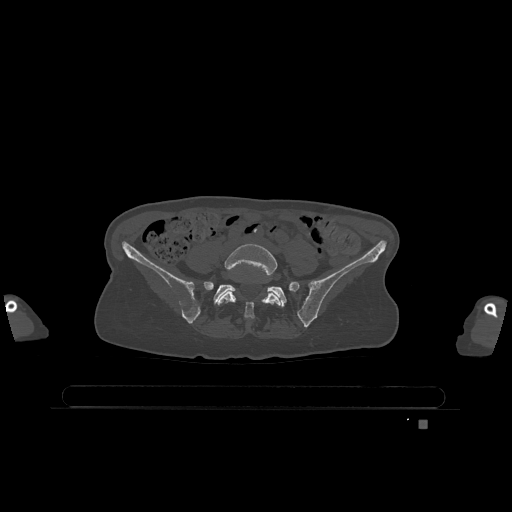
CT including the spine, one axial slice; slice 221 of 1317 in the series (ordered by position); bone window (W 1800 / L 400 HU); 512 × 512 image matrix, field of view 500 × 500 mm. Female patient, age 74 years. Case-level facts recorded for this patient, not image findings: primary cancer: lung; vertebrae with lytic lesions (as recorded): T1, T4, T5, T6, L4, L5.
Structures marked on this image (semi-automatically segmented with operator editing):
- L5 vertebra: bounding box [x1, y1, x2, y2] px = [217, 244, 281, 319]